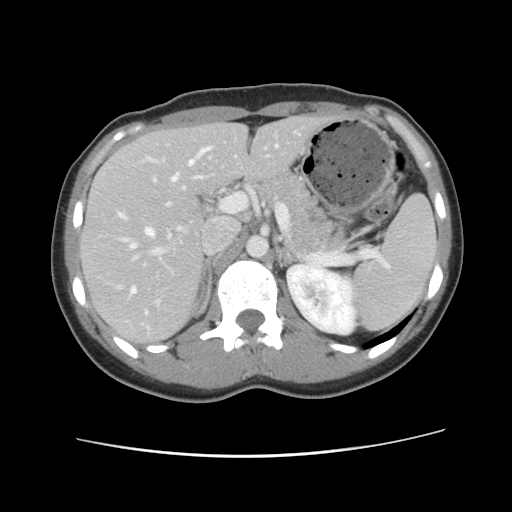
Contrast-enhanced abdominal CT, one axial slice. Position 64 of 134 along the scan axis. 120 kVp. Soft-tissue window (W 400 / L 40 HU). 2.5 mm slice thickness. 512 × 512 image matrix. Female patient, age 33 years. From the clinical record (not read from this slice): diagnosis: colorectal cancer liver metastases, imaged before liver resection; multiple liver metastases: yes; largest metastasis: 4.5 cm.
Annotated regions visible in this slice (manually delineated by an expert):
- hepatic veins: bounding box (x1, y1, x2, y2) in pixels: (118, 145, 278, 315)
- liver: (82, 116, 323, 345)
- planned liver remnant (the part of the liver to remain after resection): (81, 116, 324, 345)
- portal vein (with intrahepatic branches): (131, 195, 235, 304)